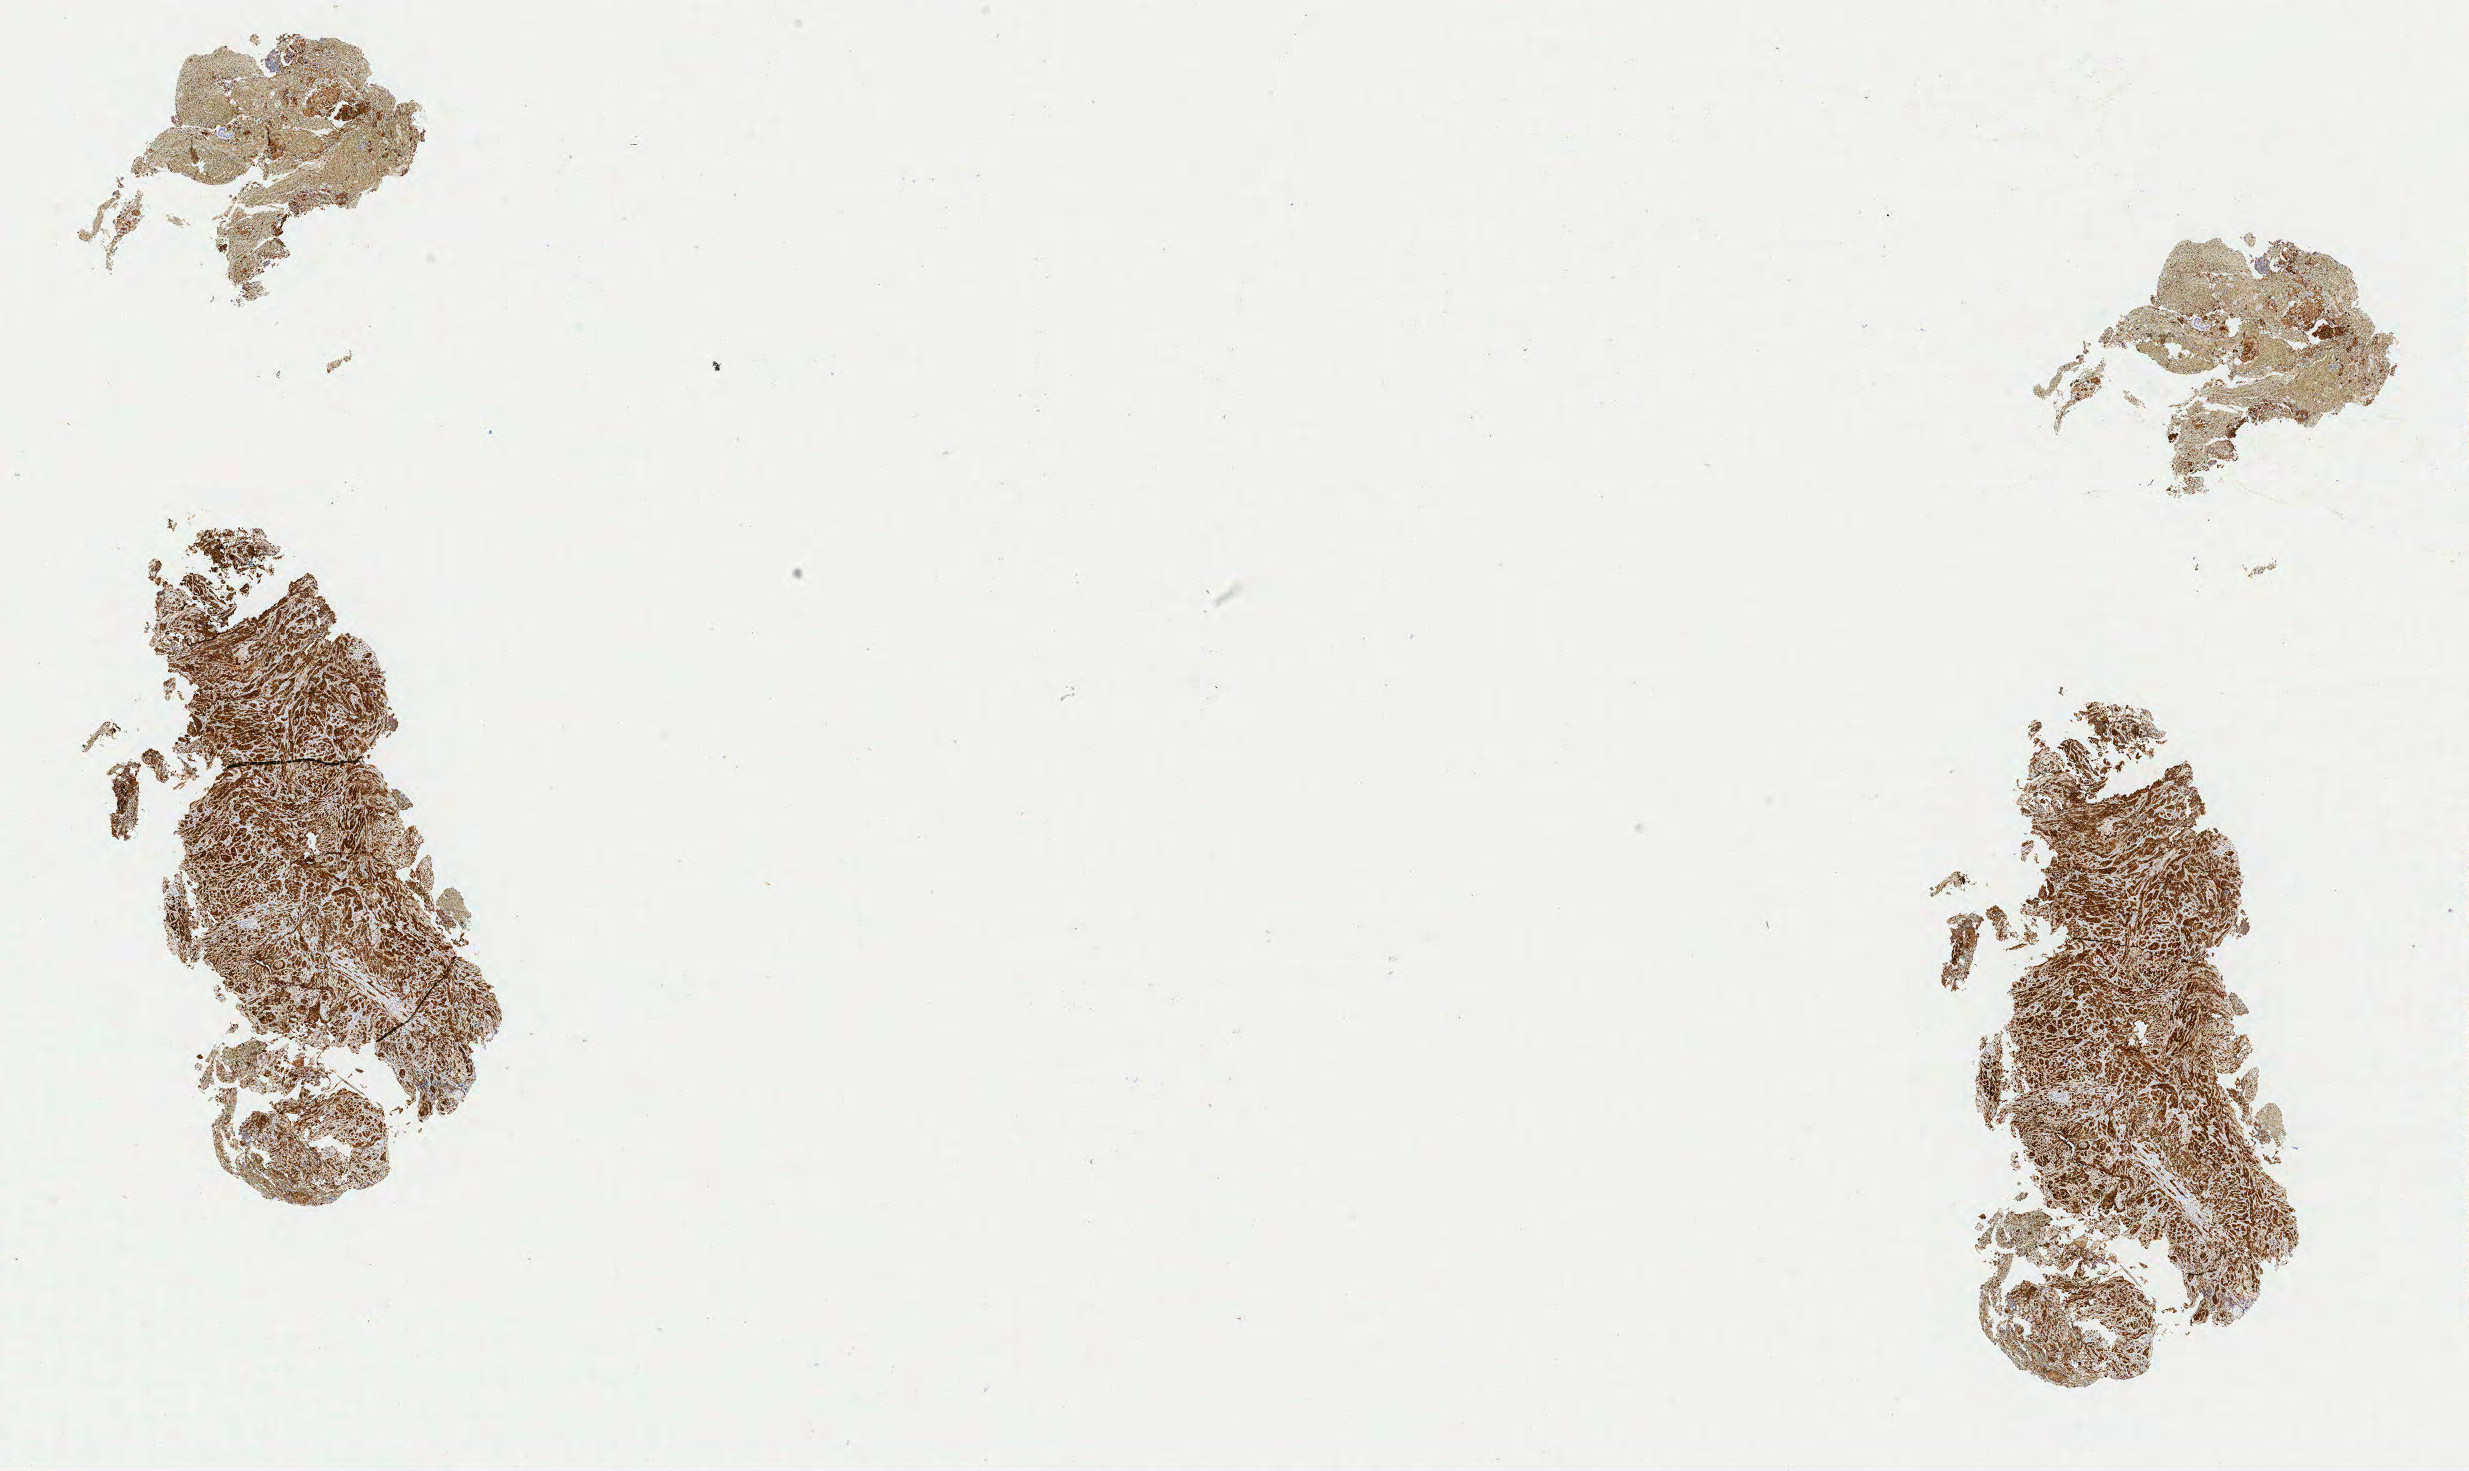
Whole-slide image, immunohistochemical stain for p16 (p16INK4a) — low-resolution overview of the scanned area, about 19.6 x 11.7 mm; tumor tissue; site: cervix. Patient female; age 42 years.
* diagnosis: Squamous cell carcinoma, keratinizing, NOS